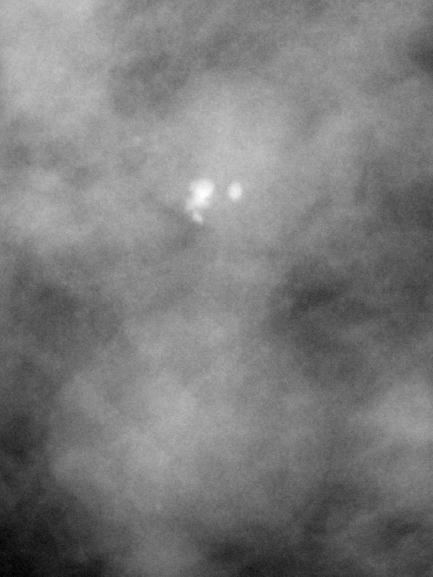
Region of interest cut from a scanned film mammogram (one marked finding), right breast, MLO view, BI-RADS breast density category 3 (scale 1–4).
- Finding: calcifications, morphology pleomorphic, distribution clustered; BI-RADS assessment category 4; pathology (as recorded): benign.